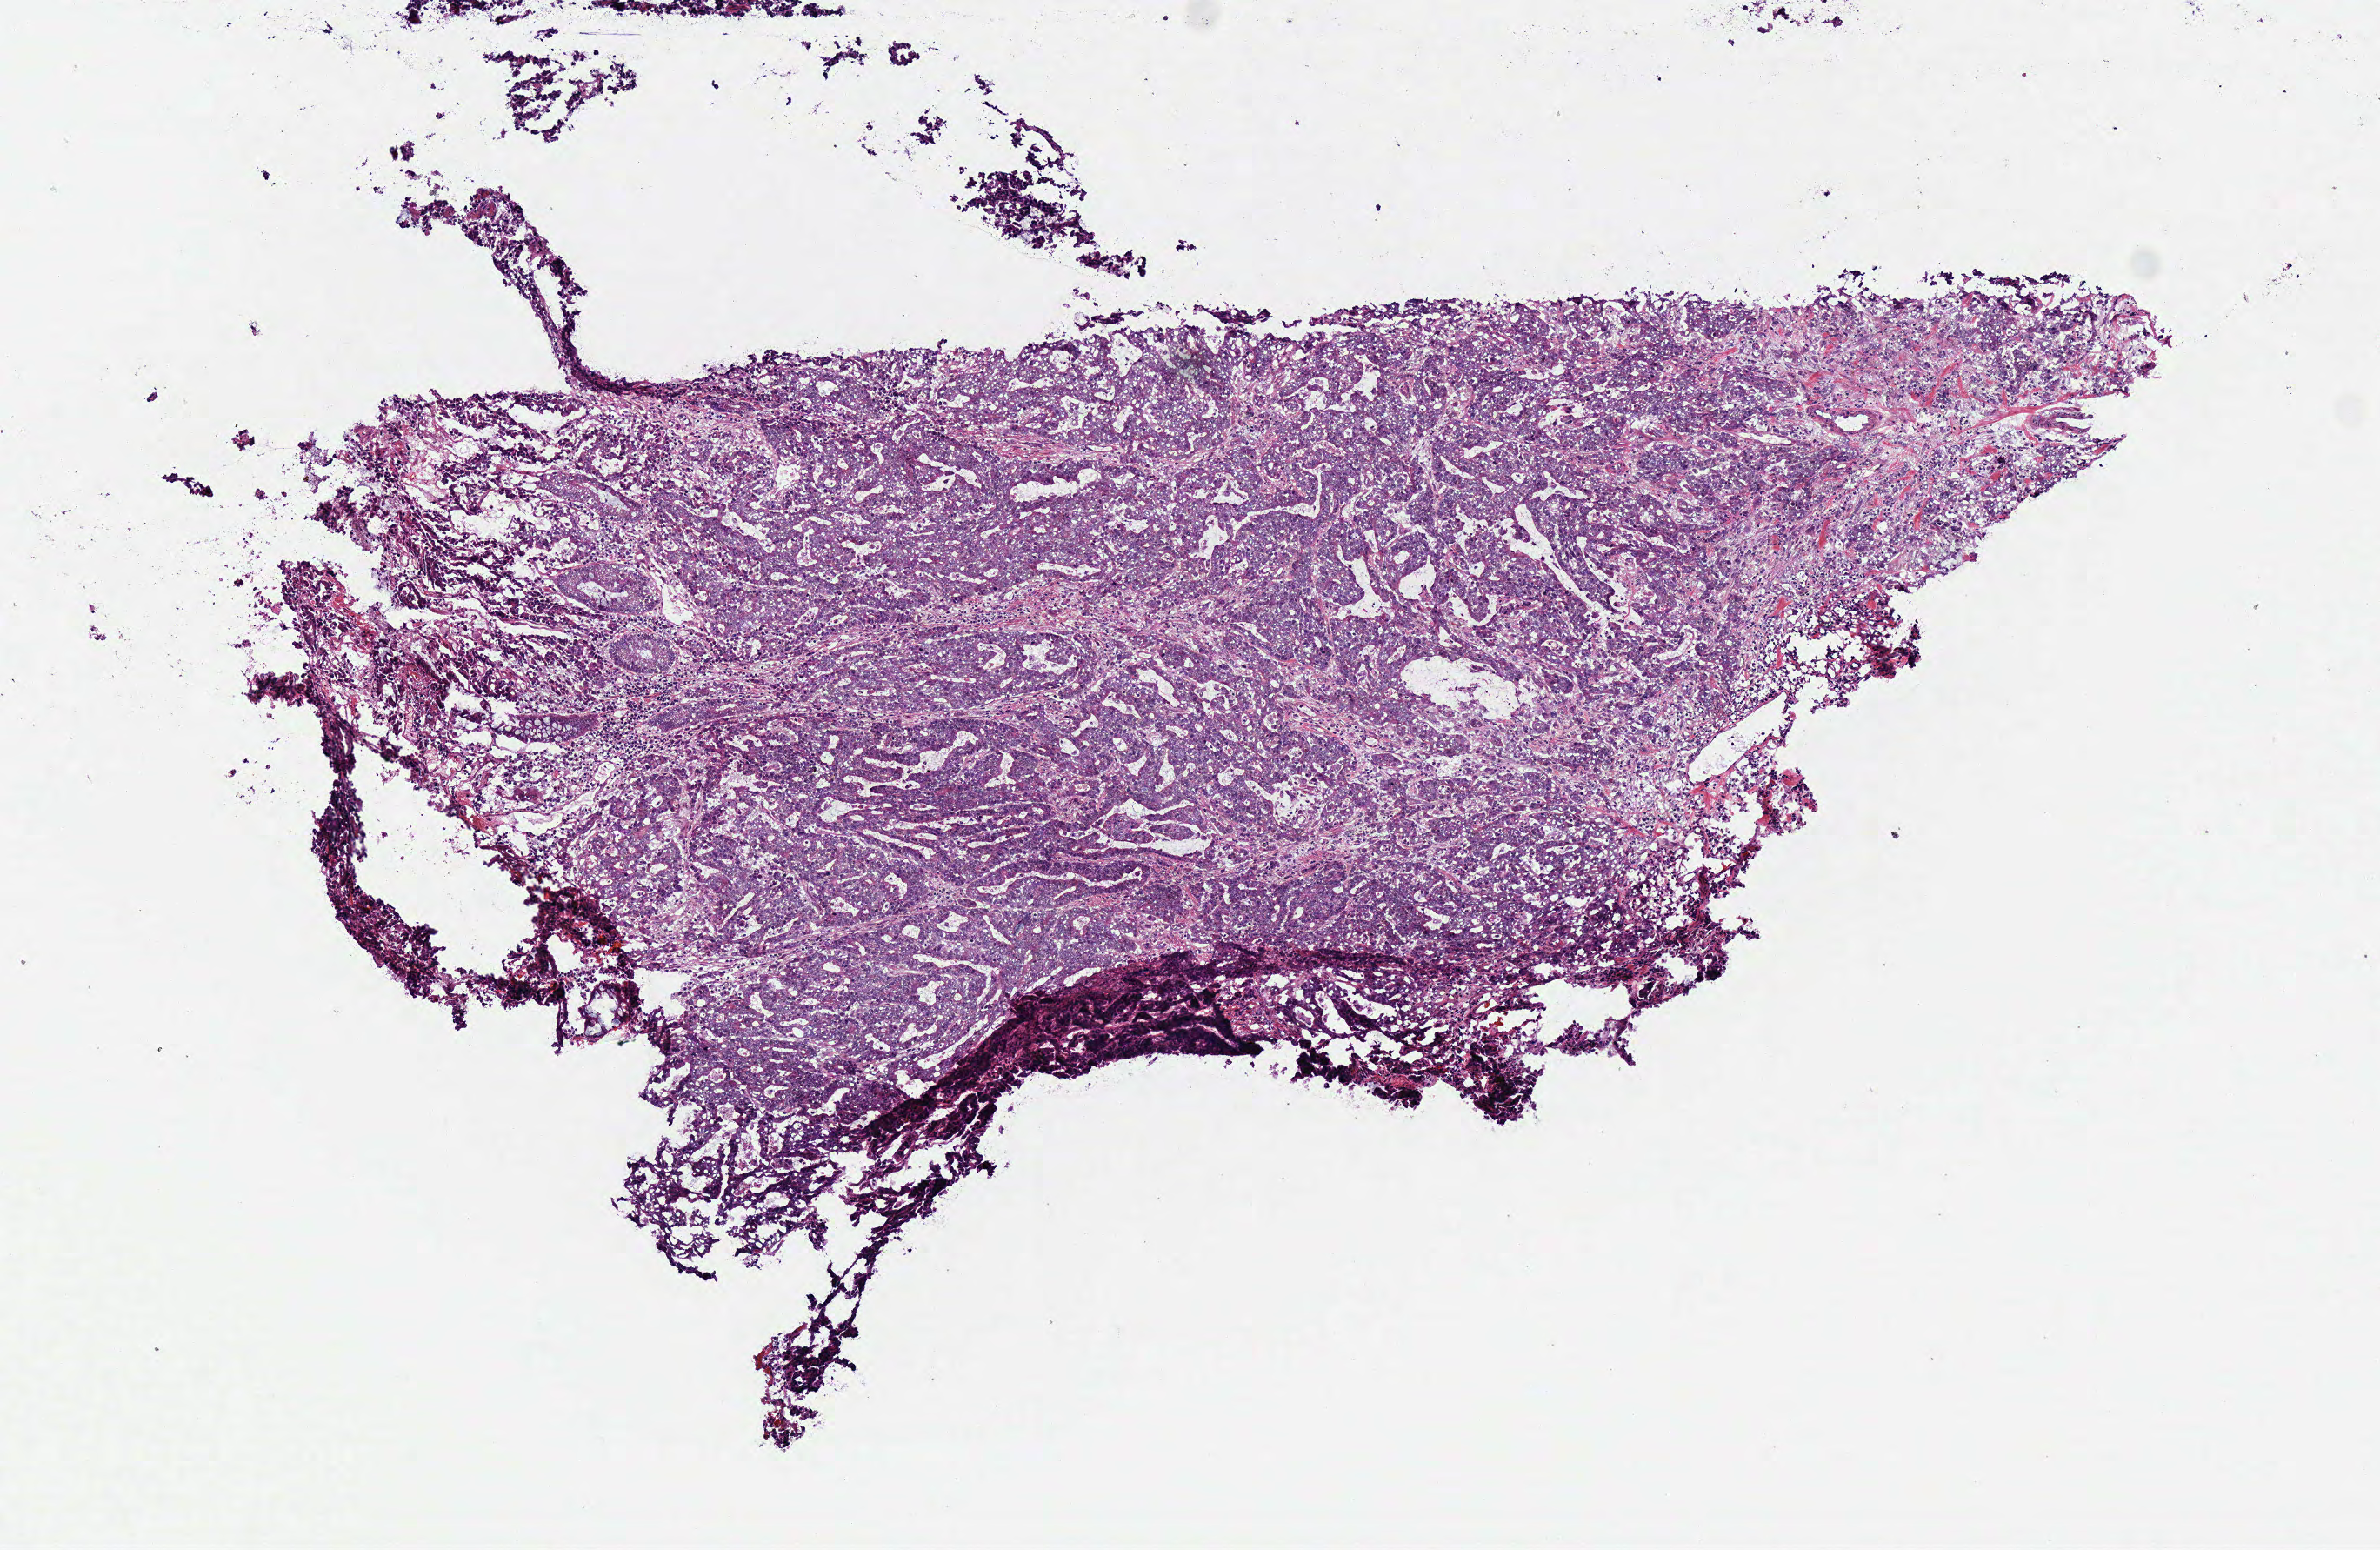
Whole-slide histology image, H&E-stained — low-resolution overview of the scanned area, about 5.4 x 3.5 mm (from a 40x scan), frozen section, primary tumour sample from the rectum. Male, age 74 years at initial diagnosis. Pathologist review of this section (percent, as recorded): tumour cells 99%, tumour nuclei 85%, normal cells 0%, stromal cells 0%, necrosis 1%. Infiltration values recorded for this section: lymphocyte infiltration 5%, monocyte infiltration 1%, neutrophil infiltration 3%.
- lymph nodes positive (case pathology): 27 of 72 examined
- pathologic diagnosis: Adenocarcinoma, NOS